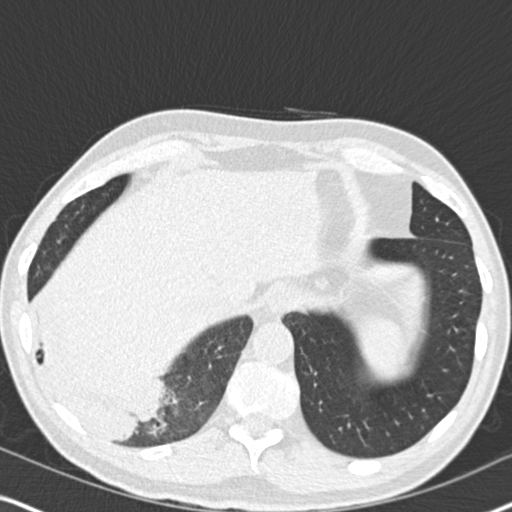
Low-dose screening chest CT, one axial slice. Slice 50 of 182 in the series (ordered by position). Lung window (W 1500 / L -600 HU). 2 mm slice thickness. 512 × 512 image matrix, field of view 330 × 330 mm.
Structures marked on this image (expert manual segmentation):
- lesion 1 (tumor, lower lobe of right lung): bounding box (x1, y1, x2, y2) in pixels: (58, 378, 154, 435)